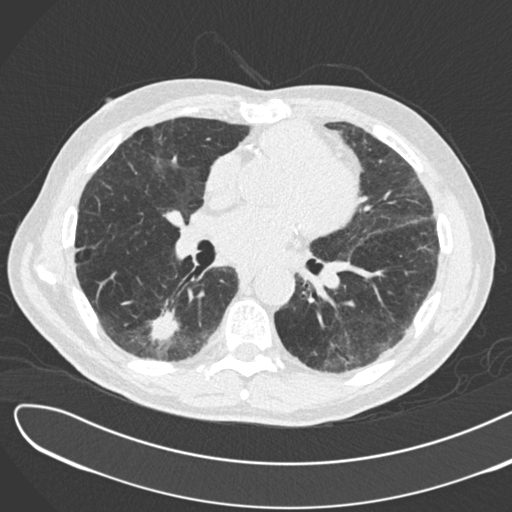
Low-dose screening chest CT, one axial slice; slice 85 of 183 in the series (ordered by position); reconstruction kernel B30f; 120 kVp; lung window (W 1500 / L -600 HU); 512 × 512 image matrix, field of view 370 × 370 mm.
Annotated regions visible in this slice (expert manual segmentation):
- lesion 1 (tumor, lower lobe of right lung): bounding box <149,308,180,344> (left, top, right, bottom; pixels)